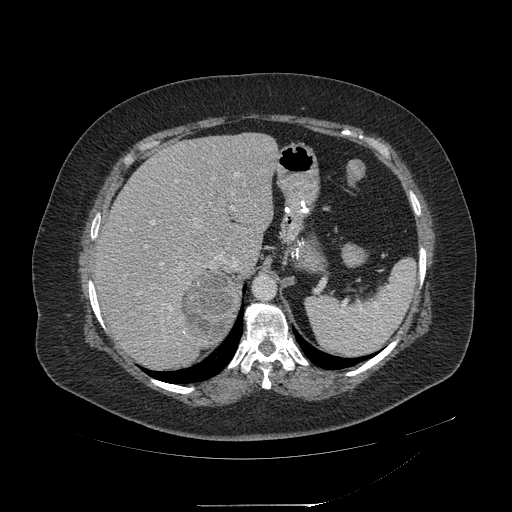
Contrast-enhanced abdominal CT, one axial slice; slice 157 of 217 in the series (ordered by position); reconstruction kernel STANDARD; intravenous contrast given; soft-tissue window (W 400 / L 40 HU); 1.25 mm slice thickness; 512 × 512 image matrix, field of view 453 × 453 mm. Female patient, age 55 years. Case-level facts recorded for this patient, not image findings: diagnosis: adrenocortical carcinoma; tumour side: right adrenal; tumour size at pathology: 11 cm; Ki-67 index: 20 %; stage (as recorded): 2.
Annotated regions visible in this slice (semi-automatic segmentation, software-assisted and operator-edited):
- mass: box from (x=182, y=273) to (x=240, y=339) px